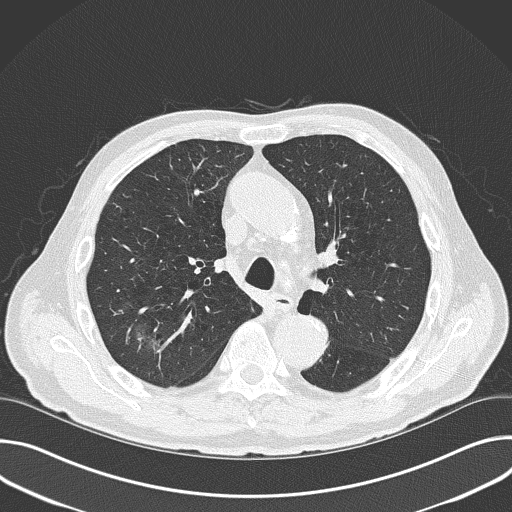
Low-dose screening chest CT, one axial slice; slice 112 of 177 in the series (ordered by position); reconstruction kernel B50f; lung window (W 1500 / L -600 HU); 512 × 512 image matrix.
Structures marked on this image (outlined manually by an expert reader):
- lesion 1 (tumor, upper lobe of right lung): bounding box [x1, y1, x2, y2] px = [136, 325, 162, 350]